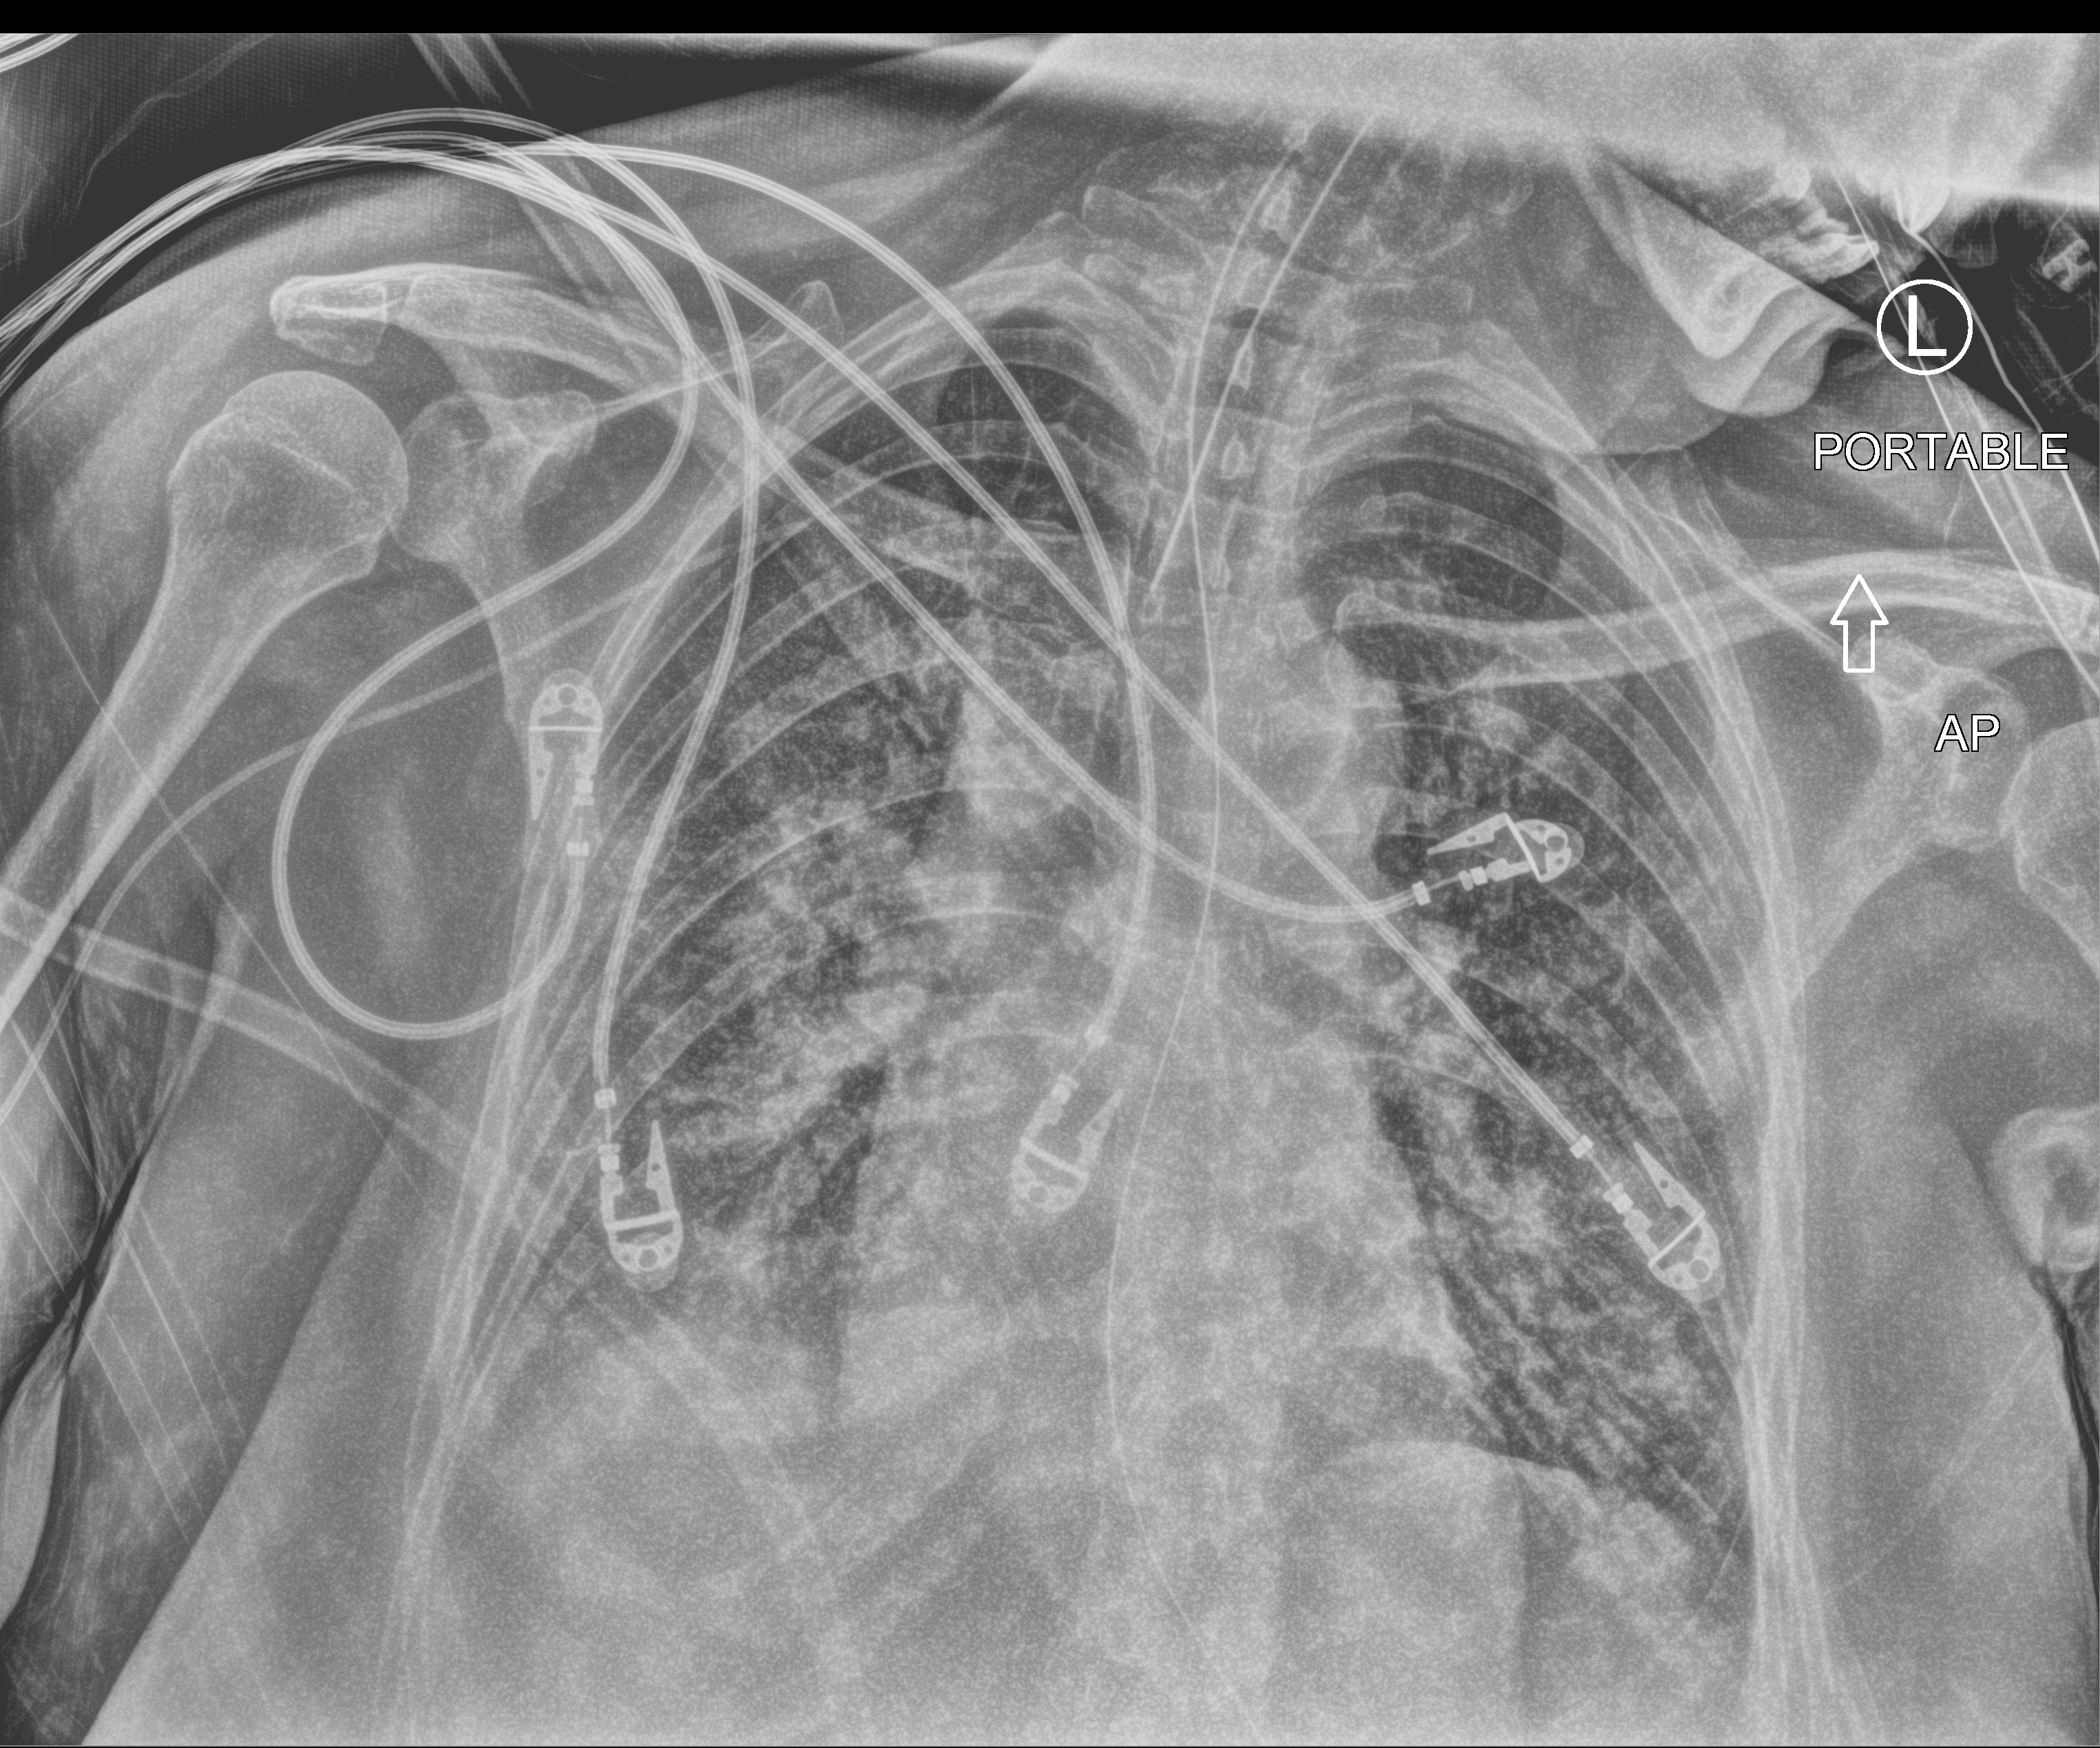
Portable chest radiograph; anteroposterior (AP) projection. Patient hospitalised with COVID-19; female, aged 18–59 years.
Hospital-stay facts (about this admission, not read from this image; timing relative to this image not recorded): mechanically ventilated during this hospital stay: yes.